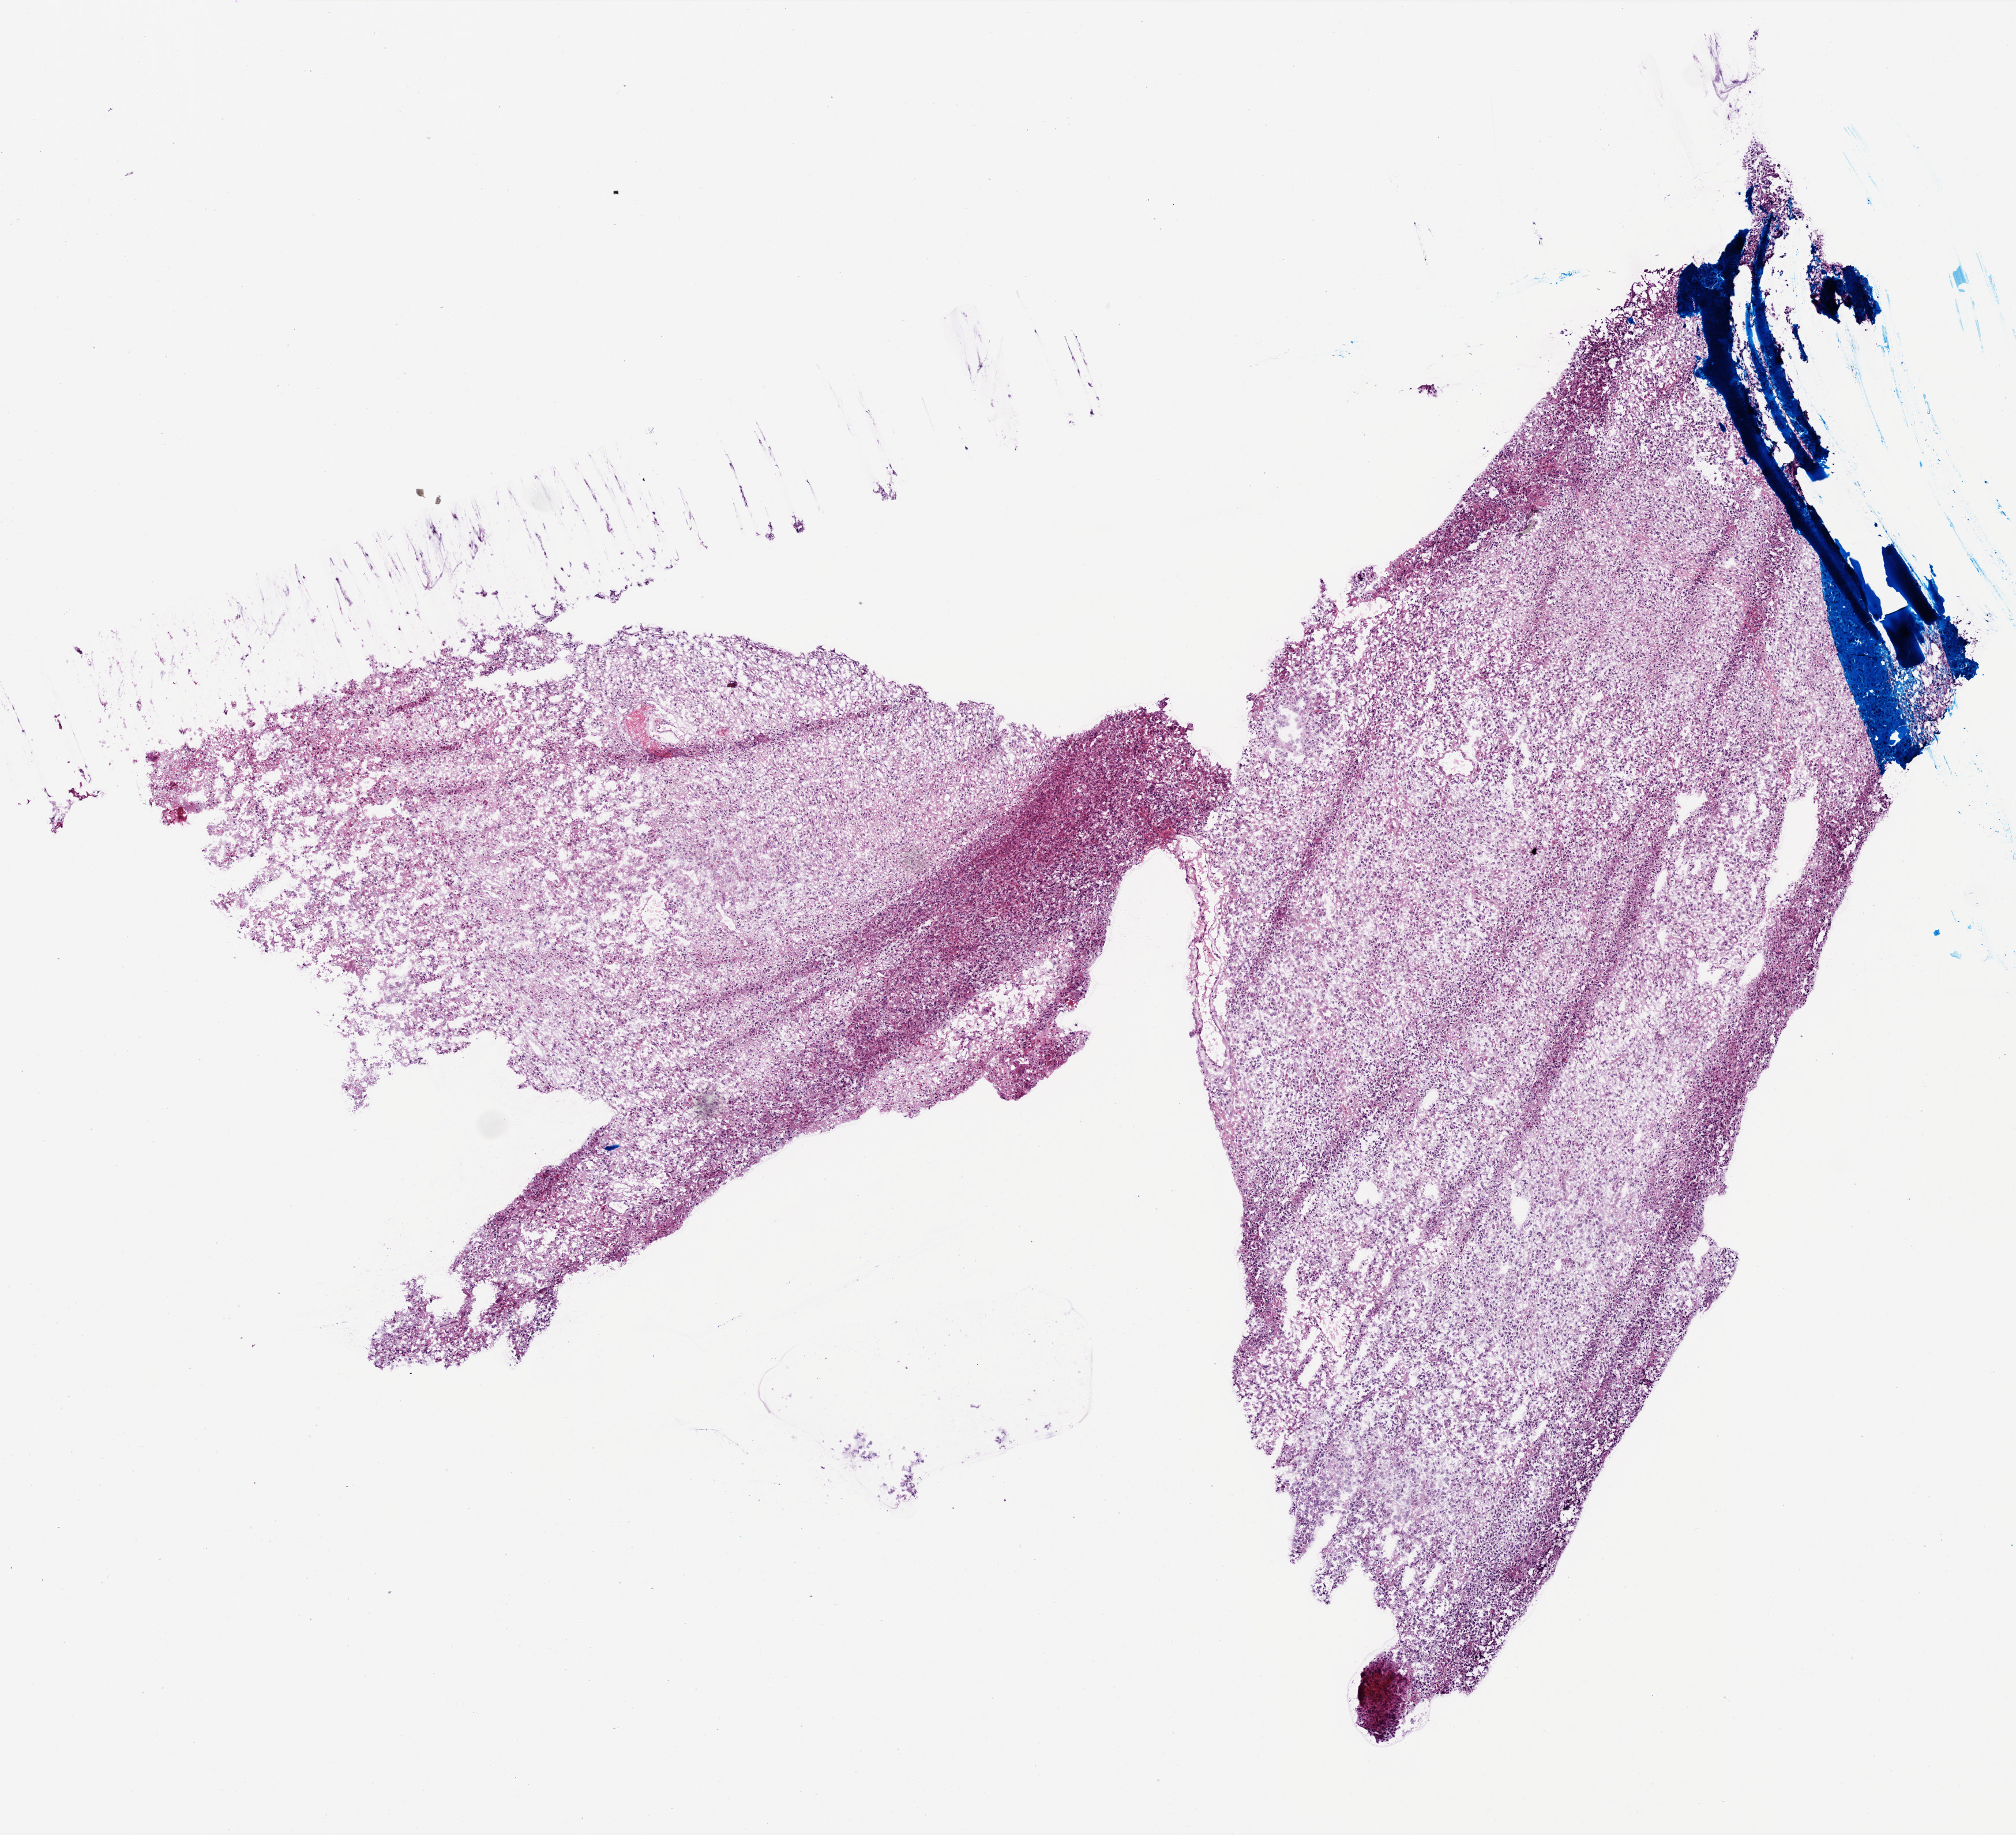
Digitized H&E tissue section (whole slide) — whole scanned area (about 7.0 x 6.4 mm) shown as a low-resolution overview; frozen section from the top of the tissue portion; sample: primary tumour, brain. Male, age 71 years at initial diagnosis. Slide review estimates, as recorded: tumour cells 90%, tumour nuclei 100%.
Diagnosis: Glioblastoma.